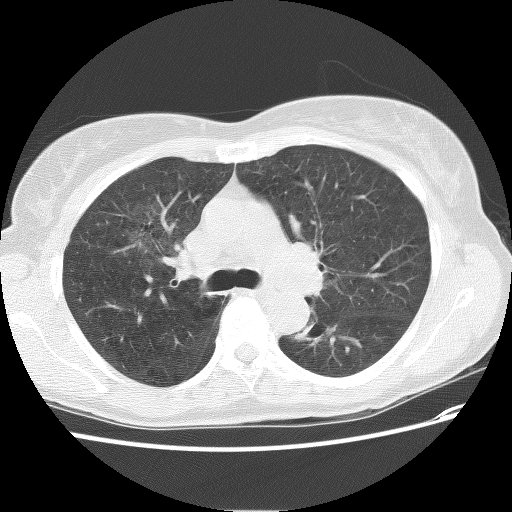
Low-dose screening chest CT, axial slice. First (baseline) screen. Lung window (W 1500 / L -600 HU). 2.5 mm slice thickness. Lung (sharp) reconstruction kernel (BONE). Slice 40 of 118 in the series. 512 × 512 image matrix, field of view 332 × 332 mm. Female, age 62 years at enrolment. Former smoker at enrolment.
• Expert reader's lesion annotation, box from (x=290, y=305) to (x=341, y=346) px.
• No non-calcified nodule or mass ≥4 mm was recorded by the screening reader at this exam.
• Official screen result: negative screen, minor abnormalities not suspicious for lung cancer.
• Lung cancer was diagnosed 898 days after this screen (after the third annual screen): squamous cell carcinoma, NOS, left lower lobe, stage IIIB (AJCC 6th edition), 31 mm at pathology.